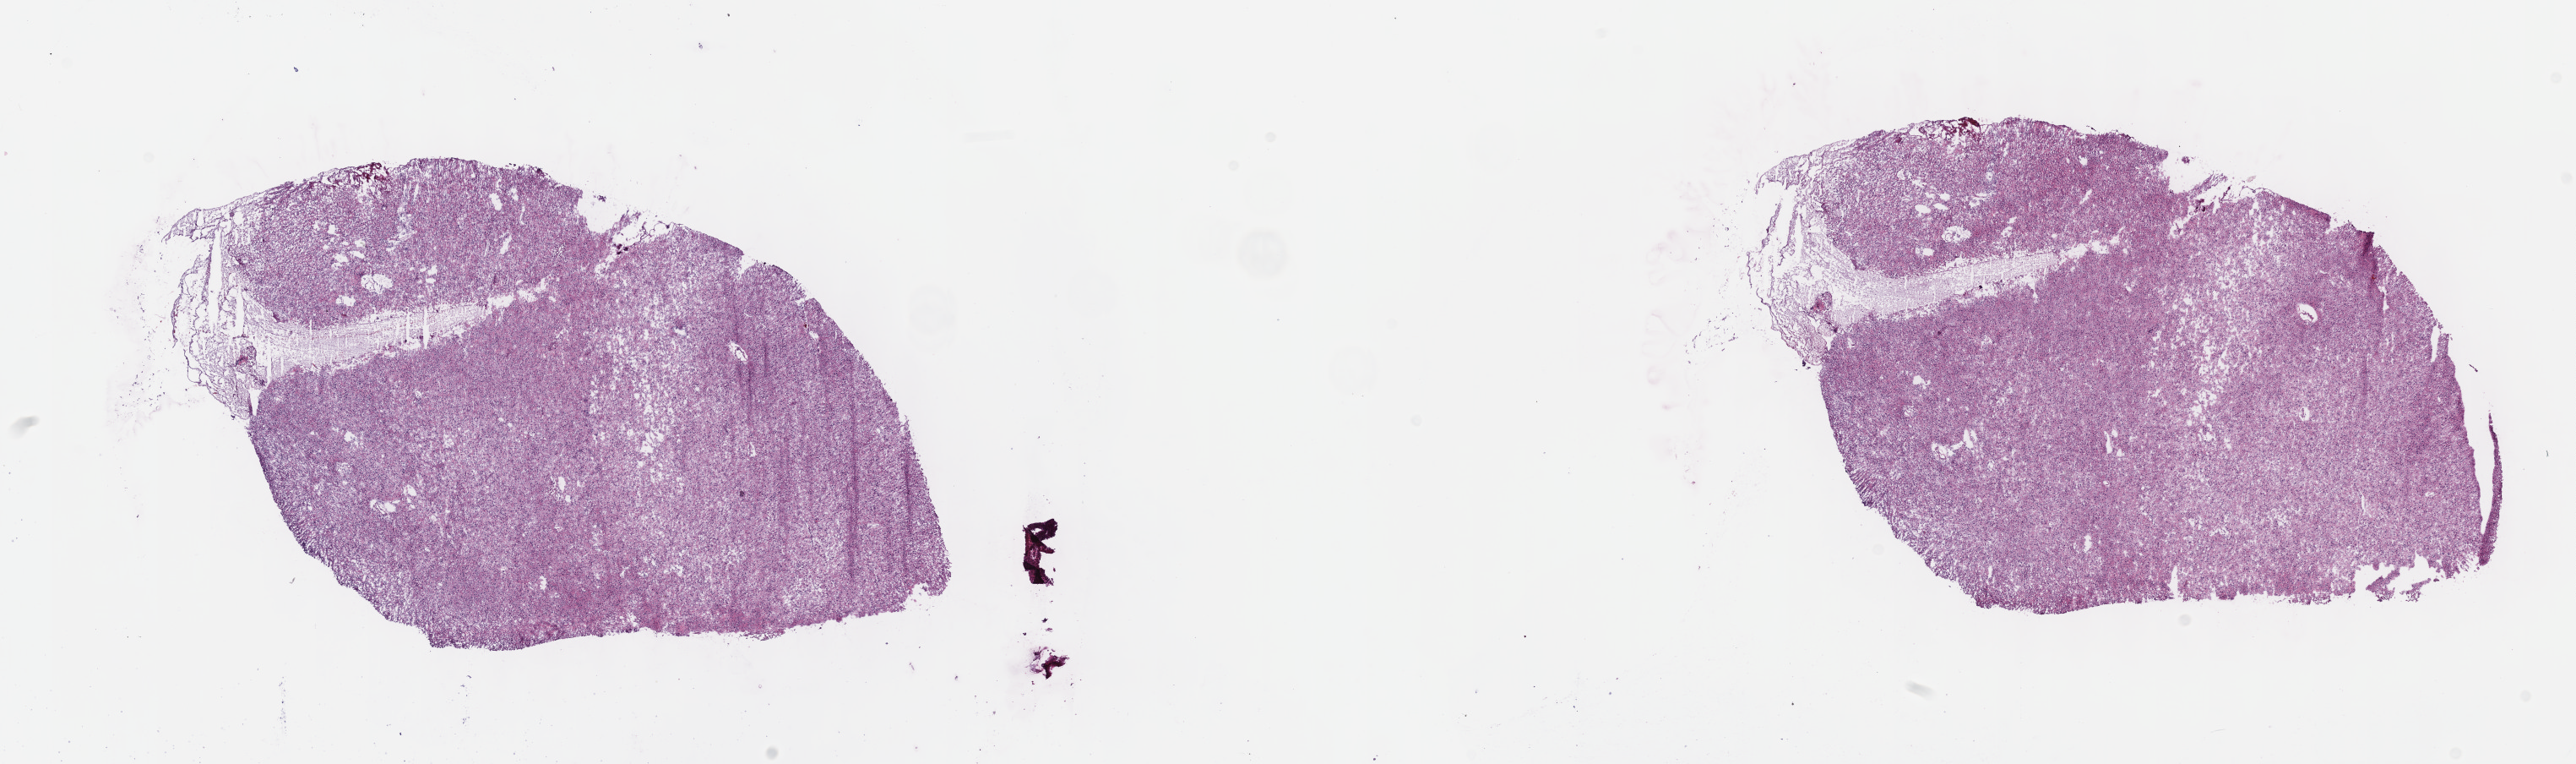
Digitized H&E tissue section (whole slide) — a low-resolution overview of the entire scanned area, about 24.7 x 7.3 mm (acquisition: 40x scan), frozen section from the top of the tissue portion, primary tumour sample from the brain. Female patient; age at initial diagnosis 46 years. Histologic grade: G2 (moderately differentiated). Pathologist review of this section (percent, as recorded): tumour cells 40%, tumour nuclei 85%, normal cells 10%, stromal cells 50%, necrosis 0%. Inflammatory infiltration, as recorded: lymphocyte infiltration 0%, monocyte infiltration 0%, neutrophil infiltration 0%.
- diagnosis: Oligodendroglioma, NOS (cerebrum)